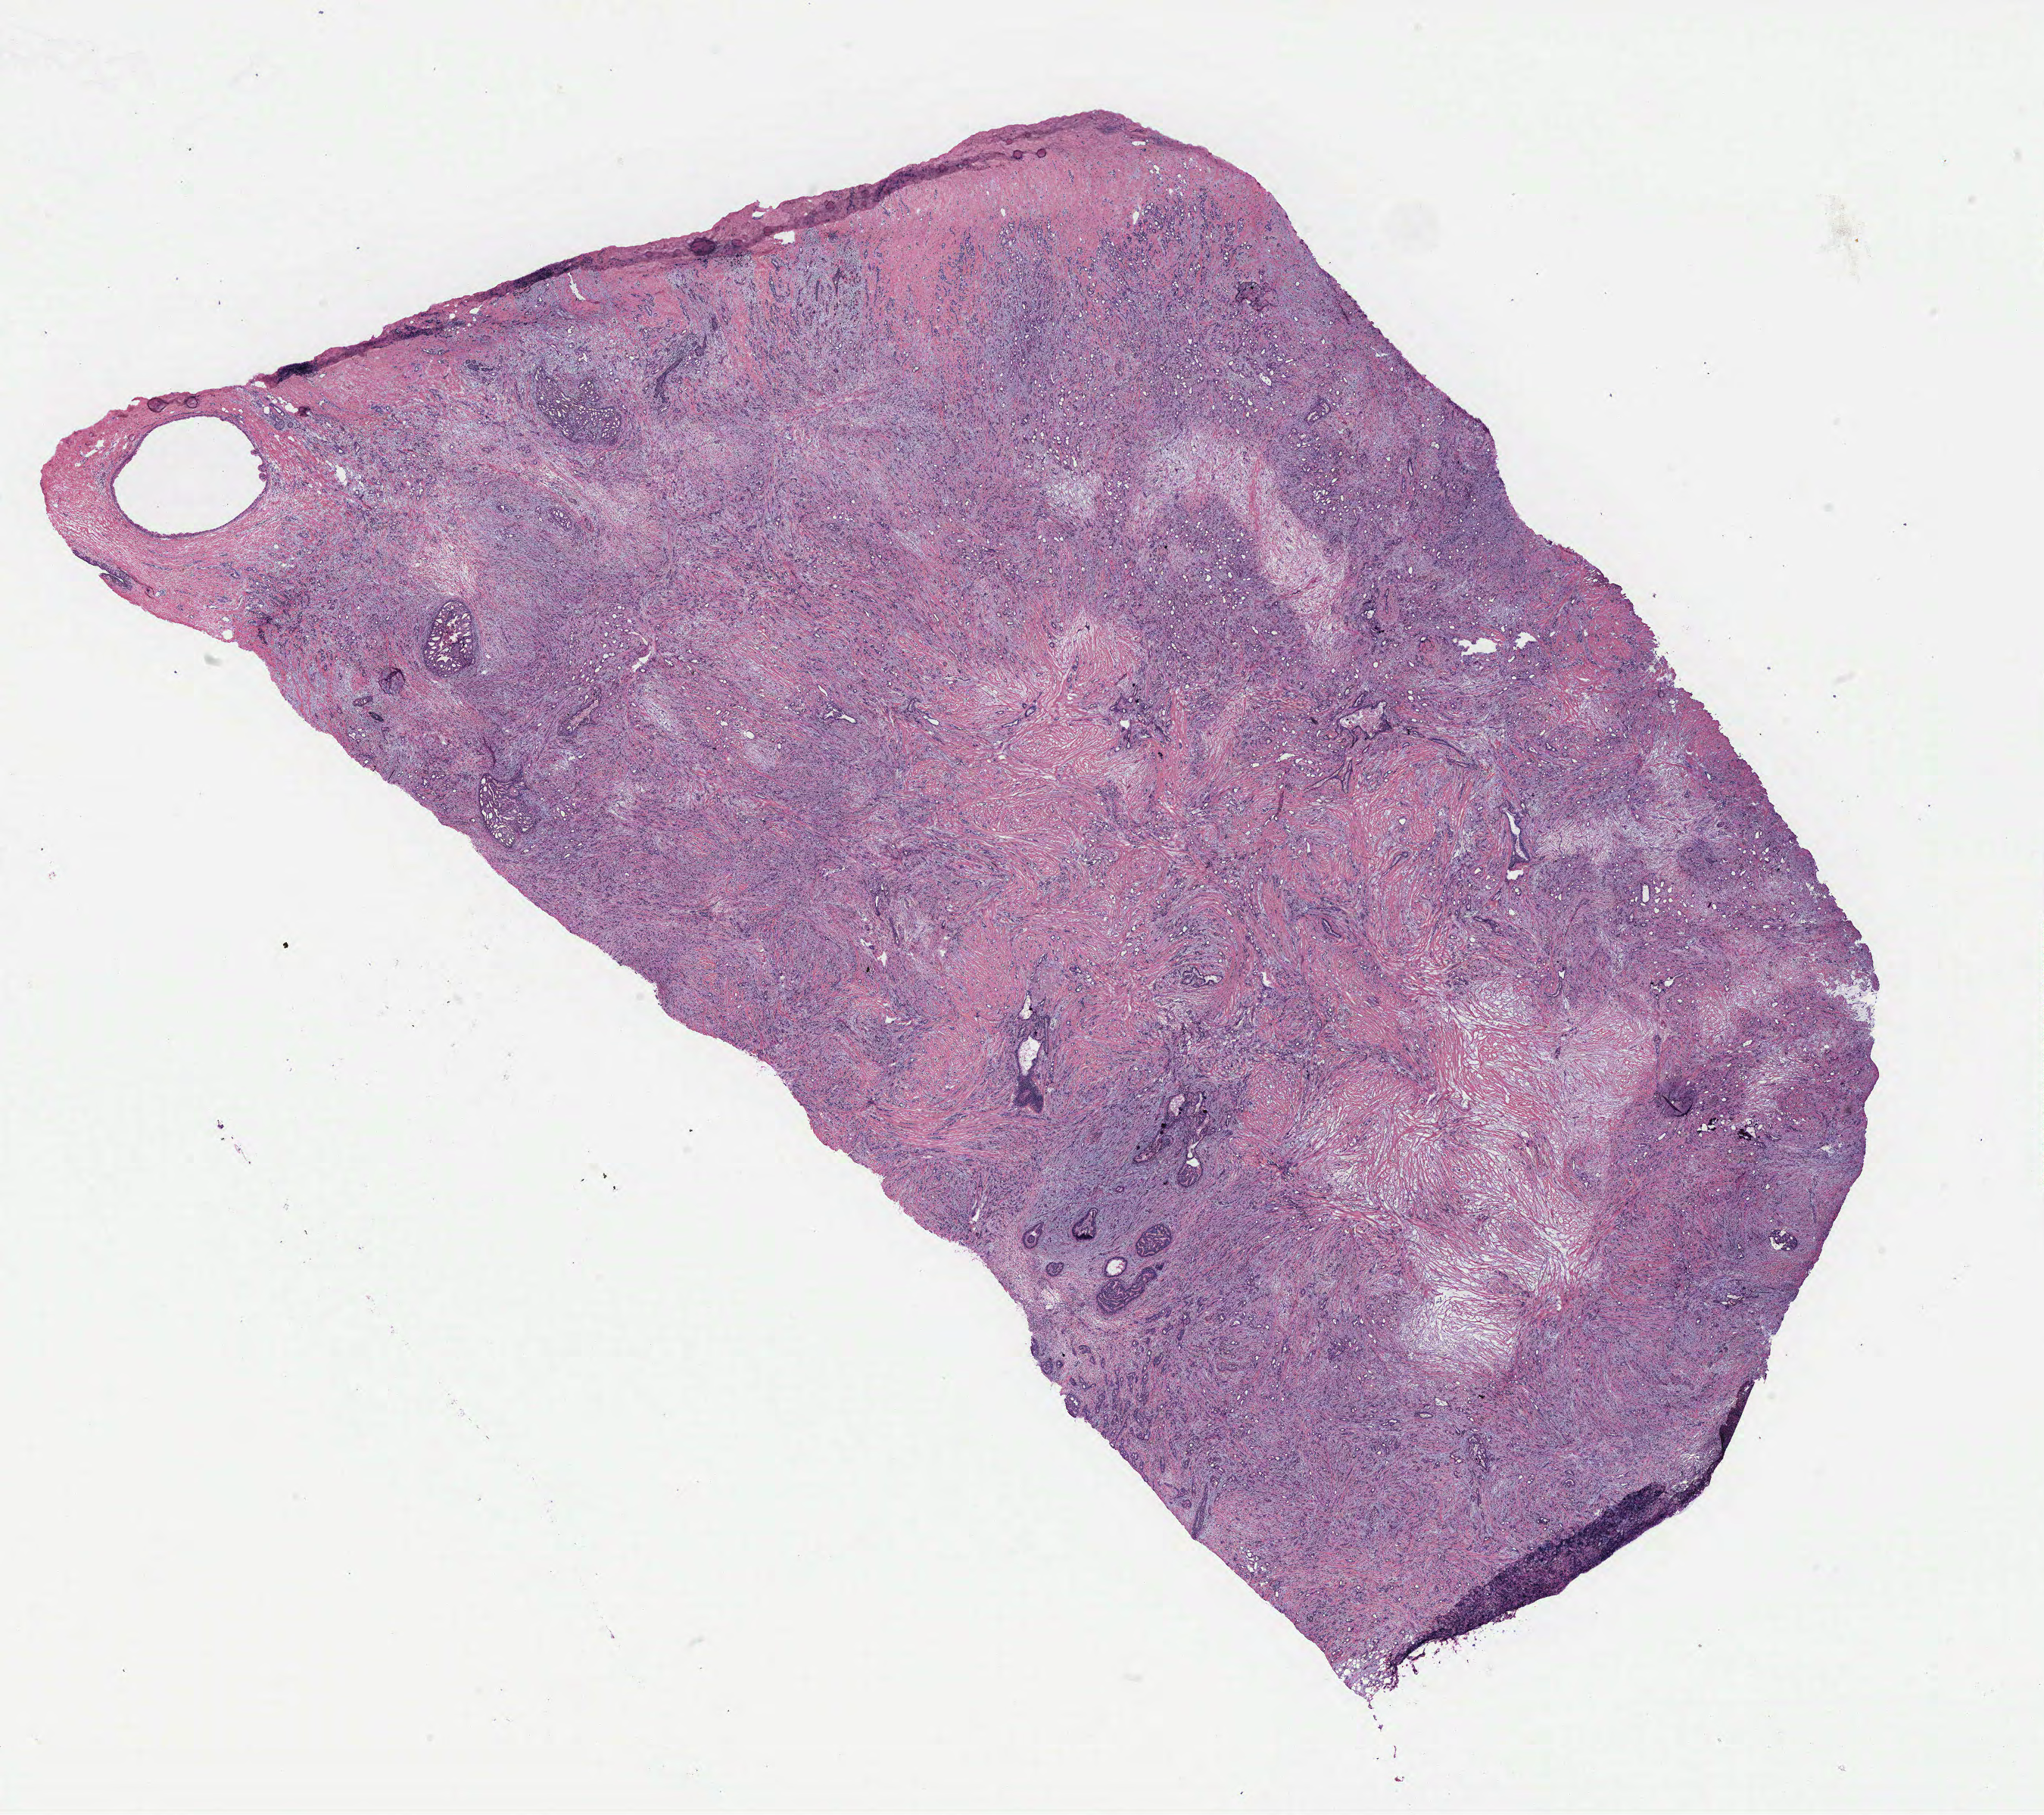
Whole-slide histology image, H&E — whole scanned area (about 21.6 x 19.2 mm, acquisition: 40x scan) shown as a low-resolution overview, breast, tumour tissue. Patient: female, age 39 years.
AJCC pathologic stage: IIIA. Histologic diagnosis: Infiltrating duct carcinoma, NOS.